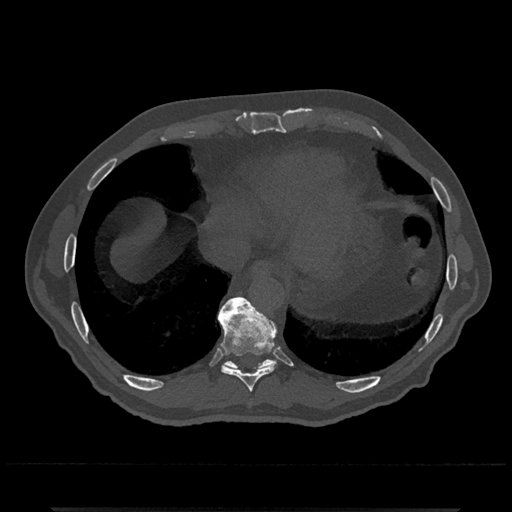
CT including the spine, one axial slice; slice 595 of 797 in the series (ordered by position); bone window (W 1800 / L 400 HU); 512 × 512 image matrix, field of view 393 × 393 mm. Male patient, age 67 years. Case-level facts recorded for this patient, not image findings: primary cancer: prostate.
Structures marked on this image (semi-automatically segmented with operator editing):
- T10 vertebra: box from (x=222, y=297) to (x=276, y=369) px
- T9 vertebra: (x=217, y=297)–(x=278, y=392)